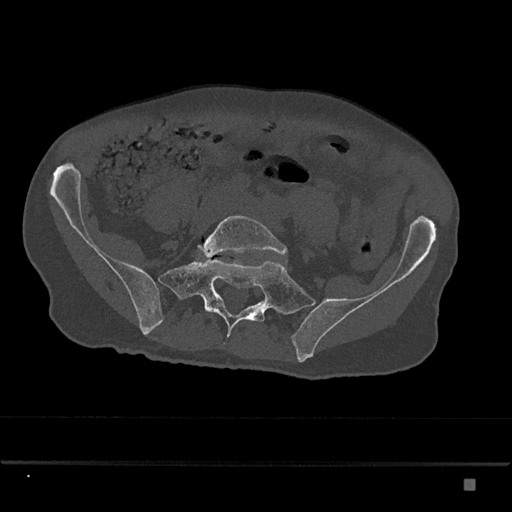
CT including the spine, one axial slice; position 237 of 797 along the scan axis; reconstruction kernel Br40s/3; 120 kVp; bone window (W 1800 / L 400 HU); 512 × 512 image matrix, field of view 390 × 390 mm. Male patient, age 72 years. From the clinical record (not read from this slice): primary cancer: prostate.
Annotated regions visible in this slice (semi-automatic segmentation, software-assisted and operator-edited):
- L5 vertebra: bounding box <199,215,288,257> (left, top, right, bottom; pixels)